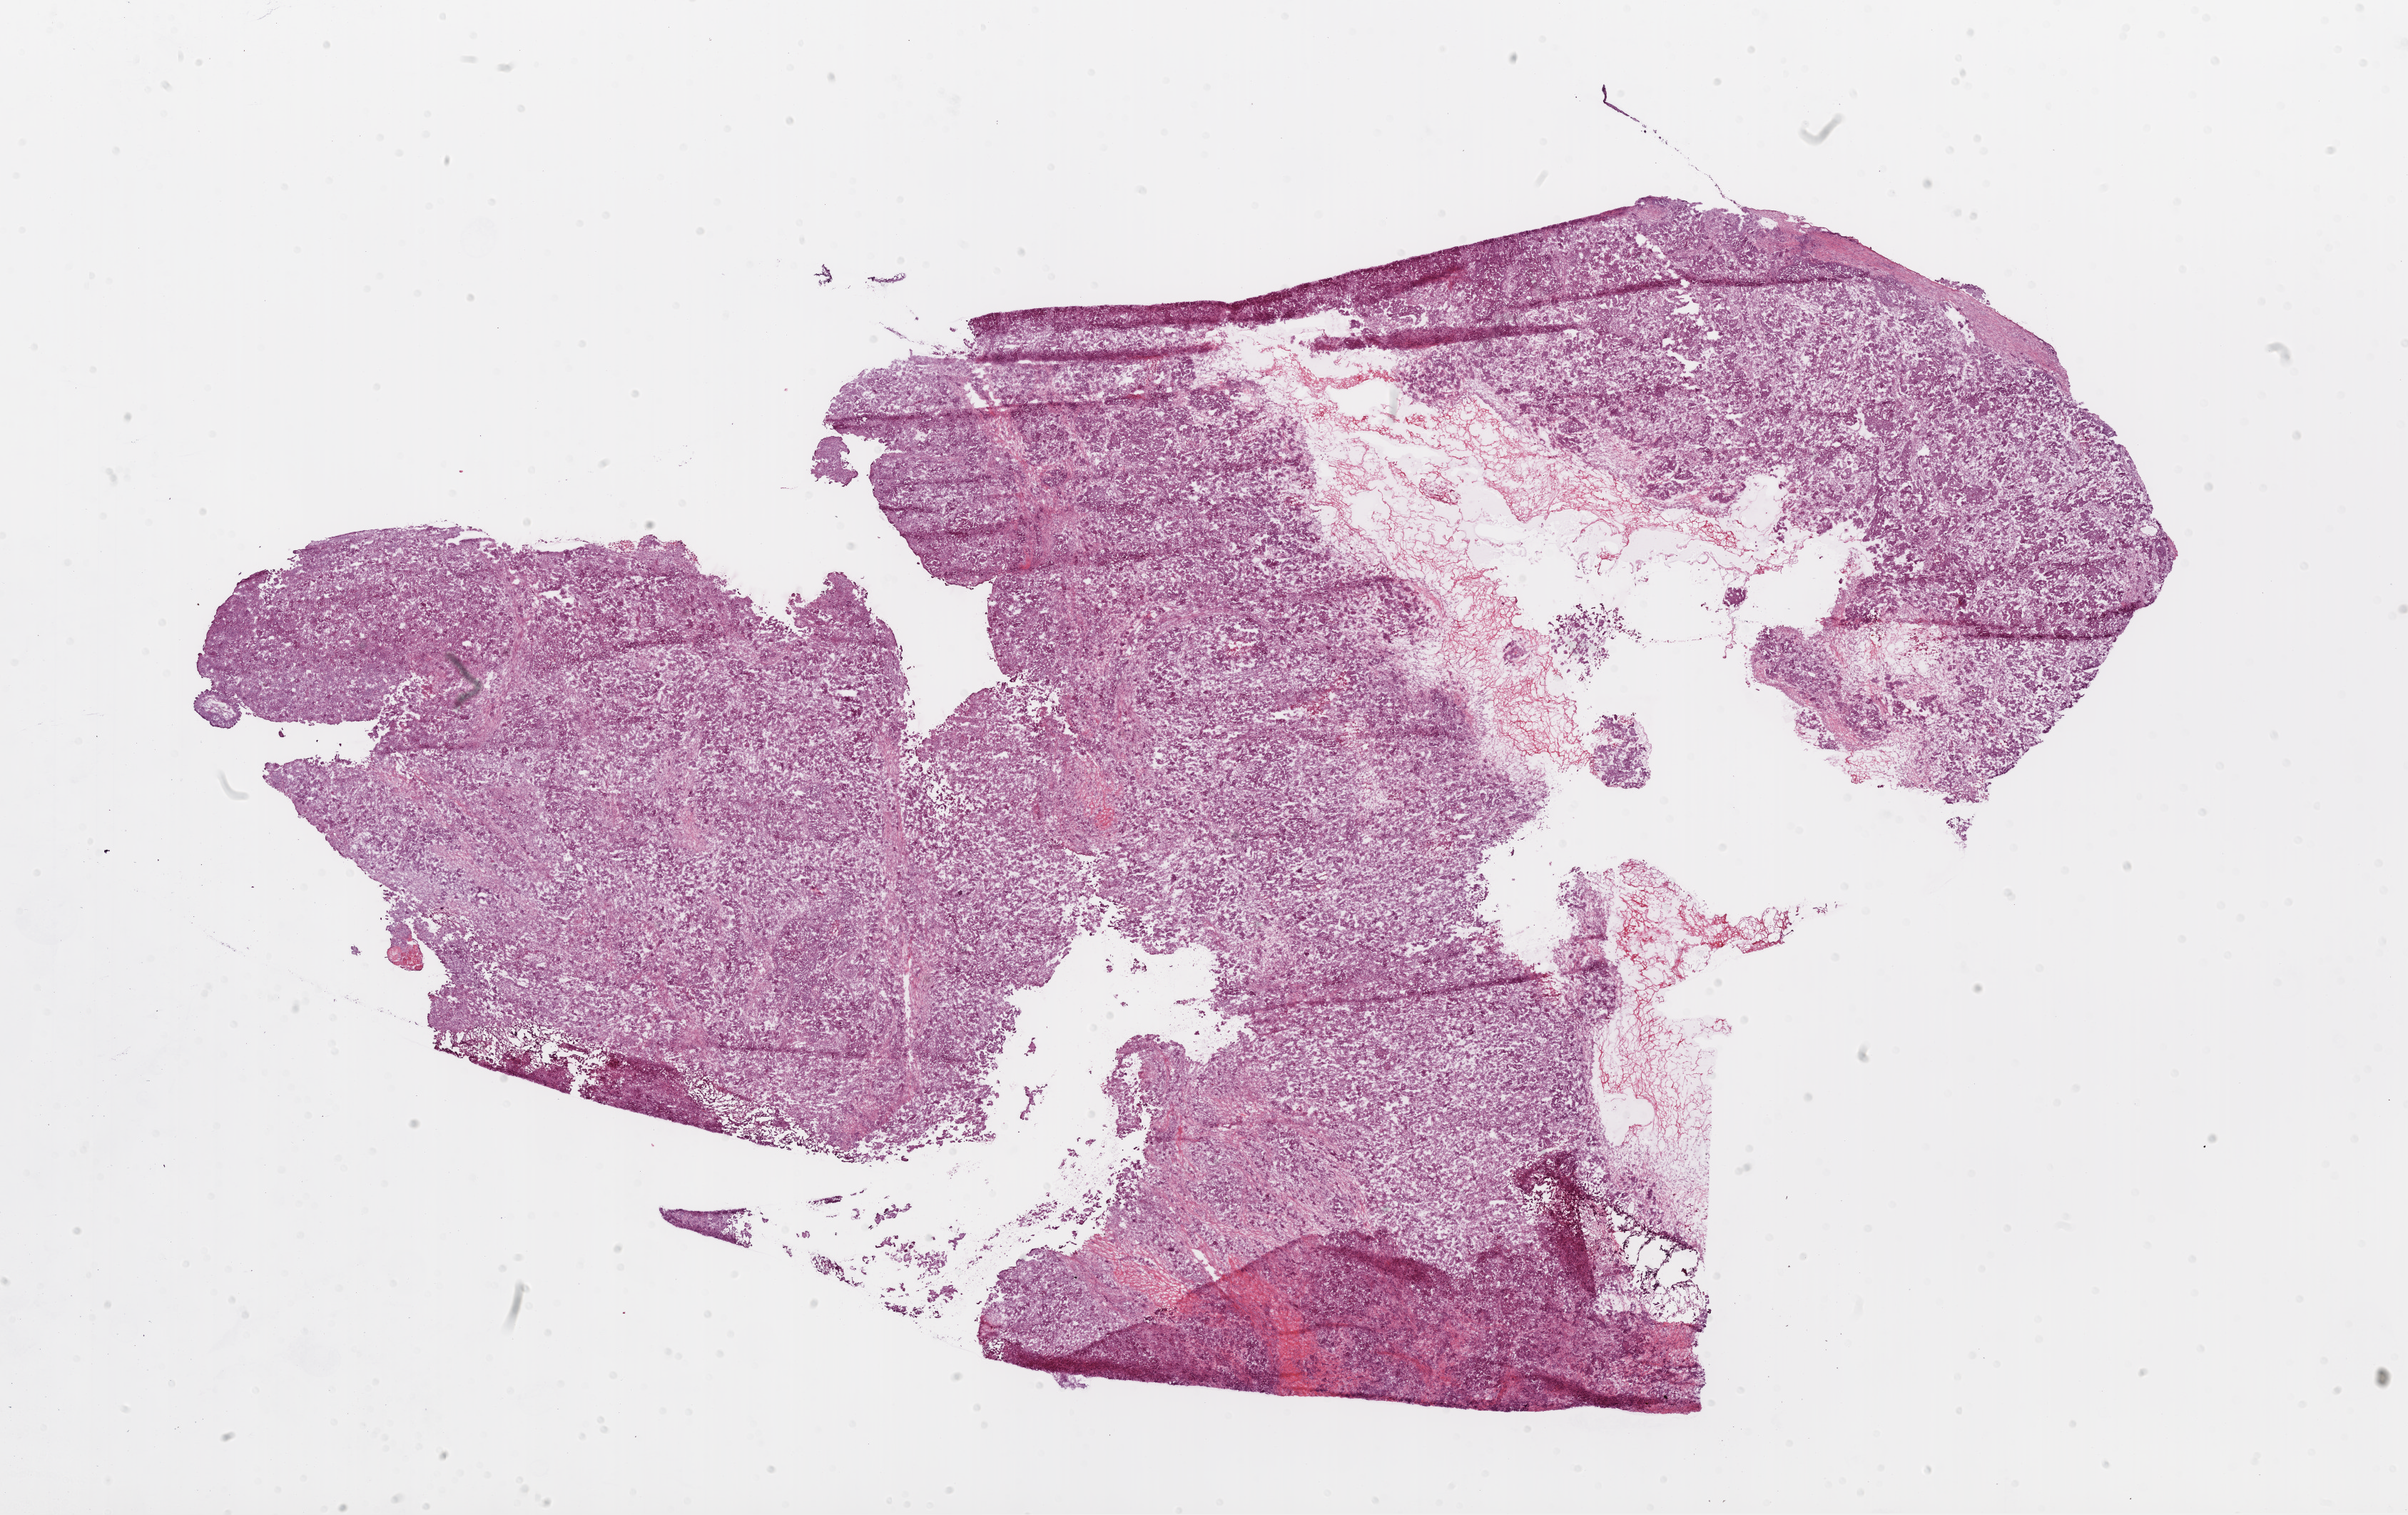
Digitized H&E tissue section (whole slide), low-resolution overview of the scanned area, about 27.1 x 17.0 mm (slide scanned at 20x). Frozen section. Sample: primary tumour, ovary. Female patient; age at initial diagnosis 65 years. Histologic grade: G3 (poorly differentiated). Pathologist review of this section (percent, as recorded): tumour cells 94%, tumour nuclei 95%, normal cells 0%, stromal cells 5%, necrosis 1%.
Histologic diagnosis: Serous cystadenocarcinoma, NOS. FIGO stage: IIIC.